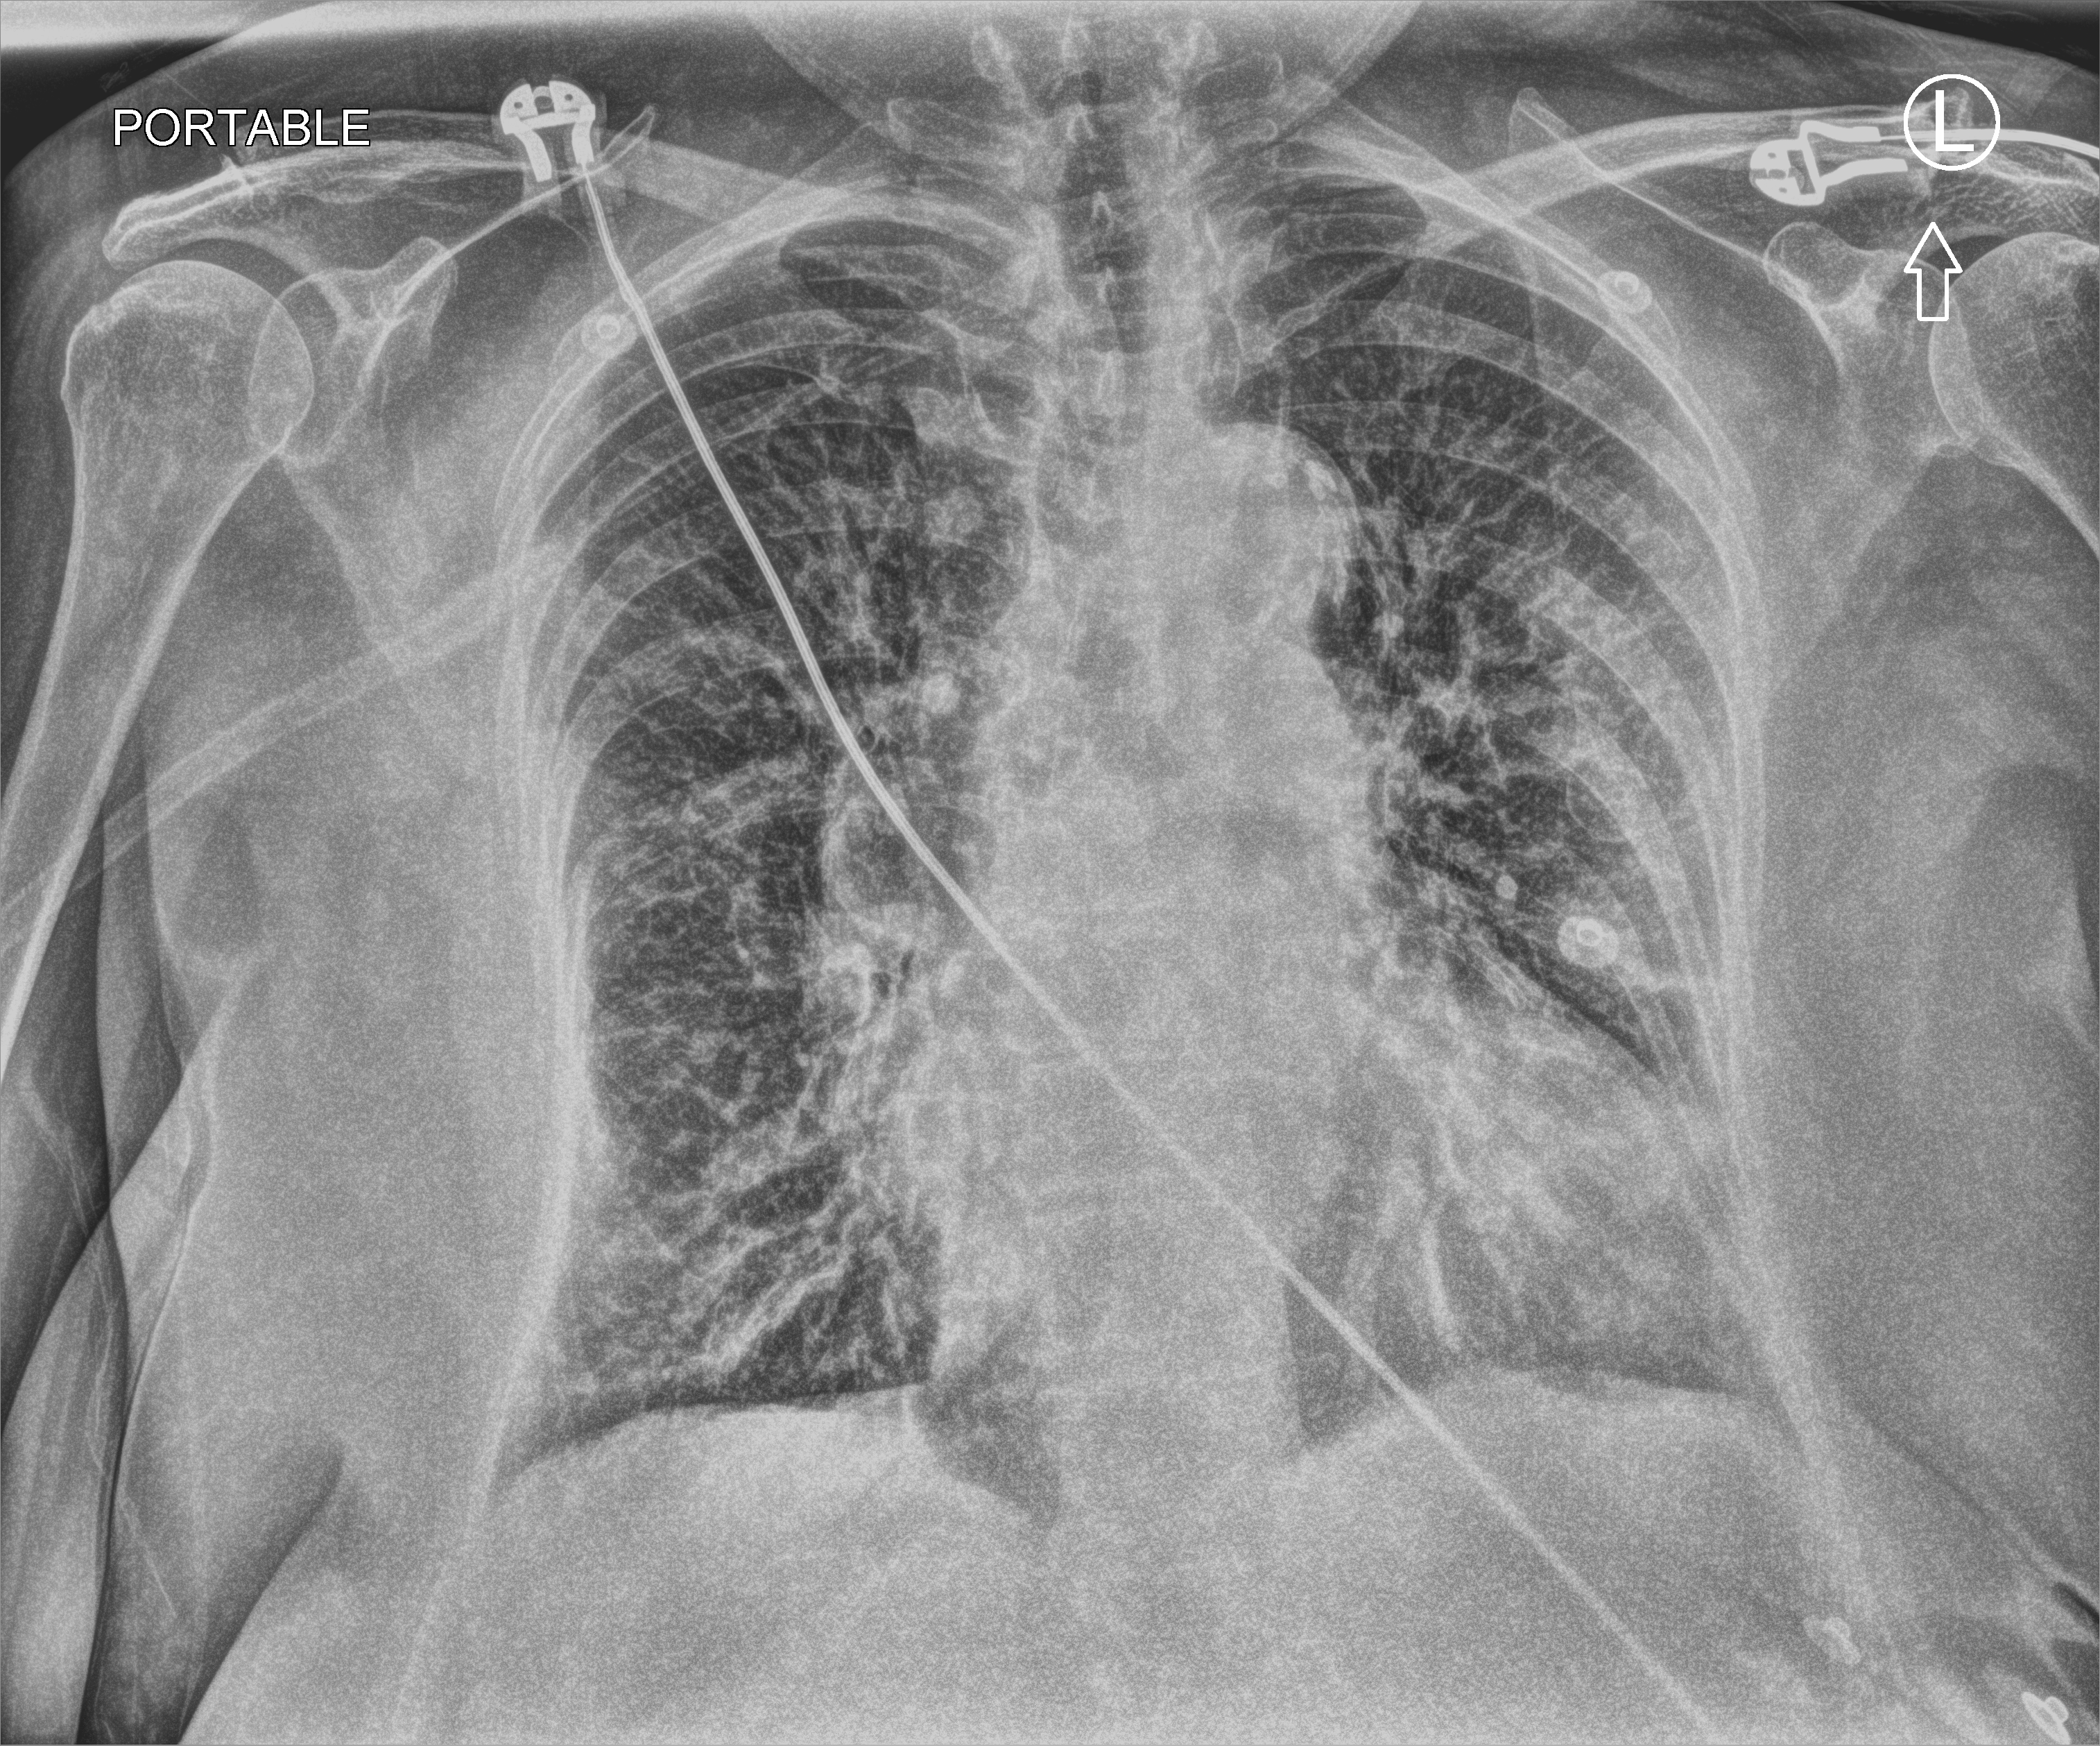
Portable chest radiograph. Patient hospitalised with COVID-19; female, aged 75–90 years.
Admission-level facts for this patient (not findings on this image; timing relative to this image not recorded):
- admitted to intensive care during this hospital stay: no
- mechanically ventilated during this hospital stay: no